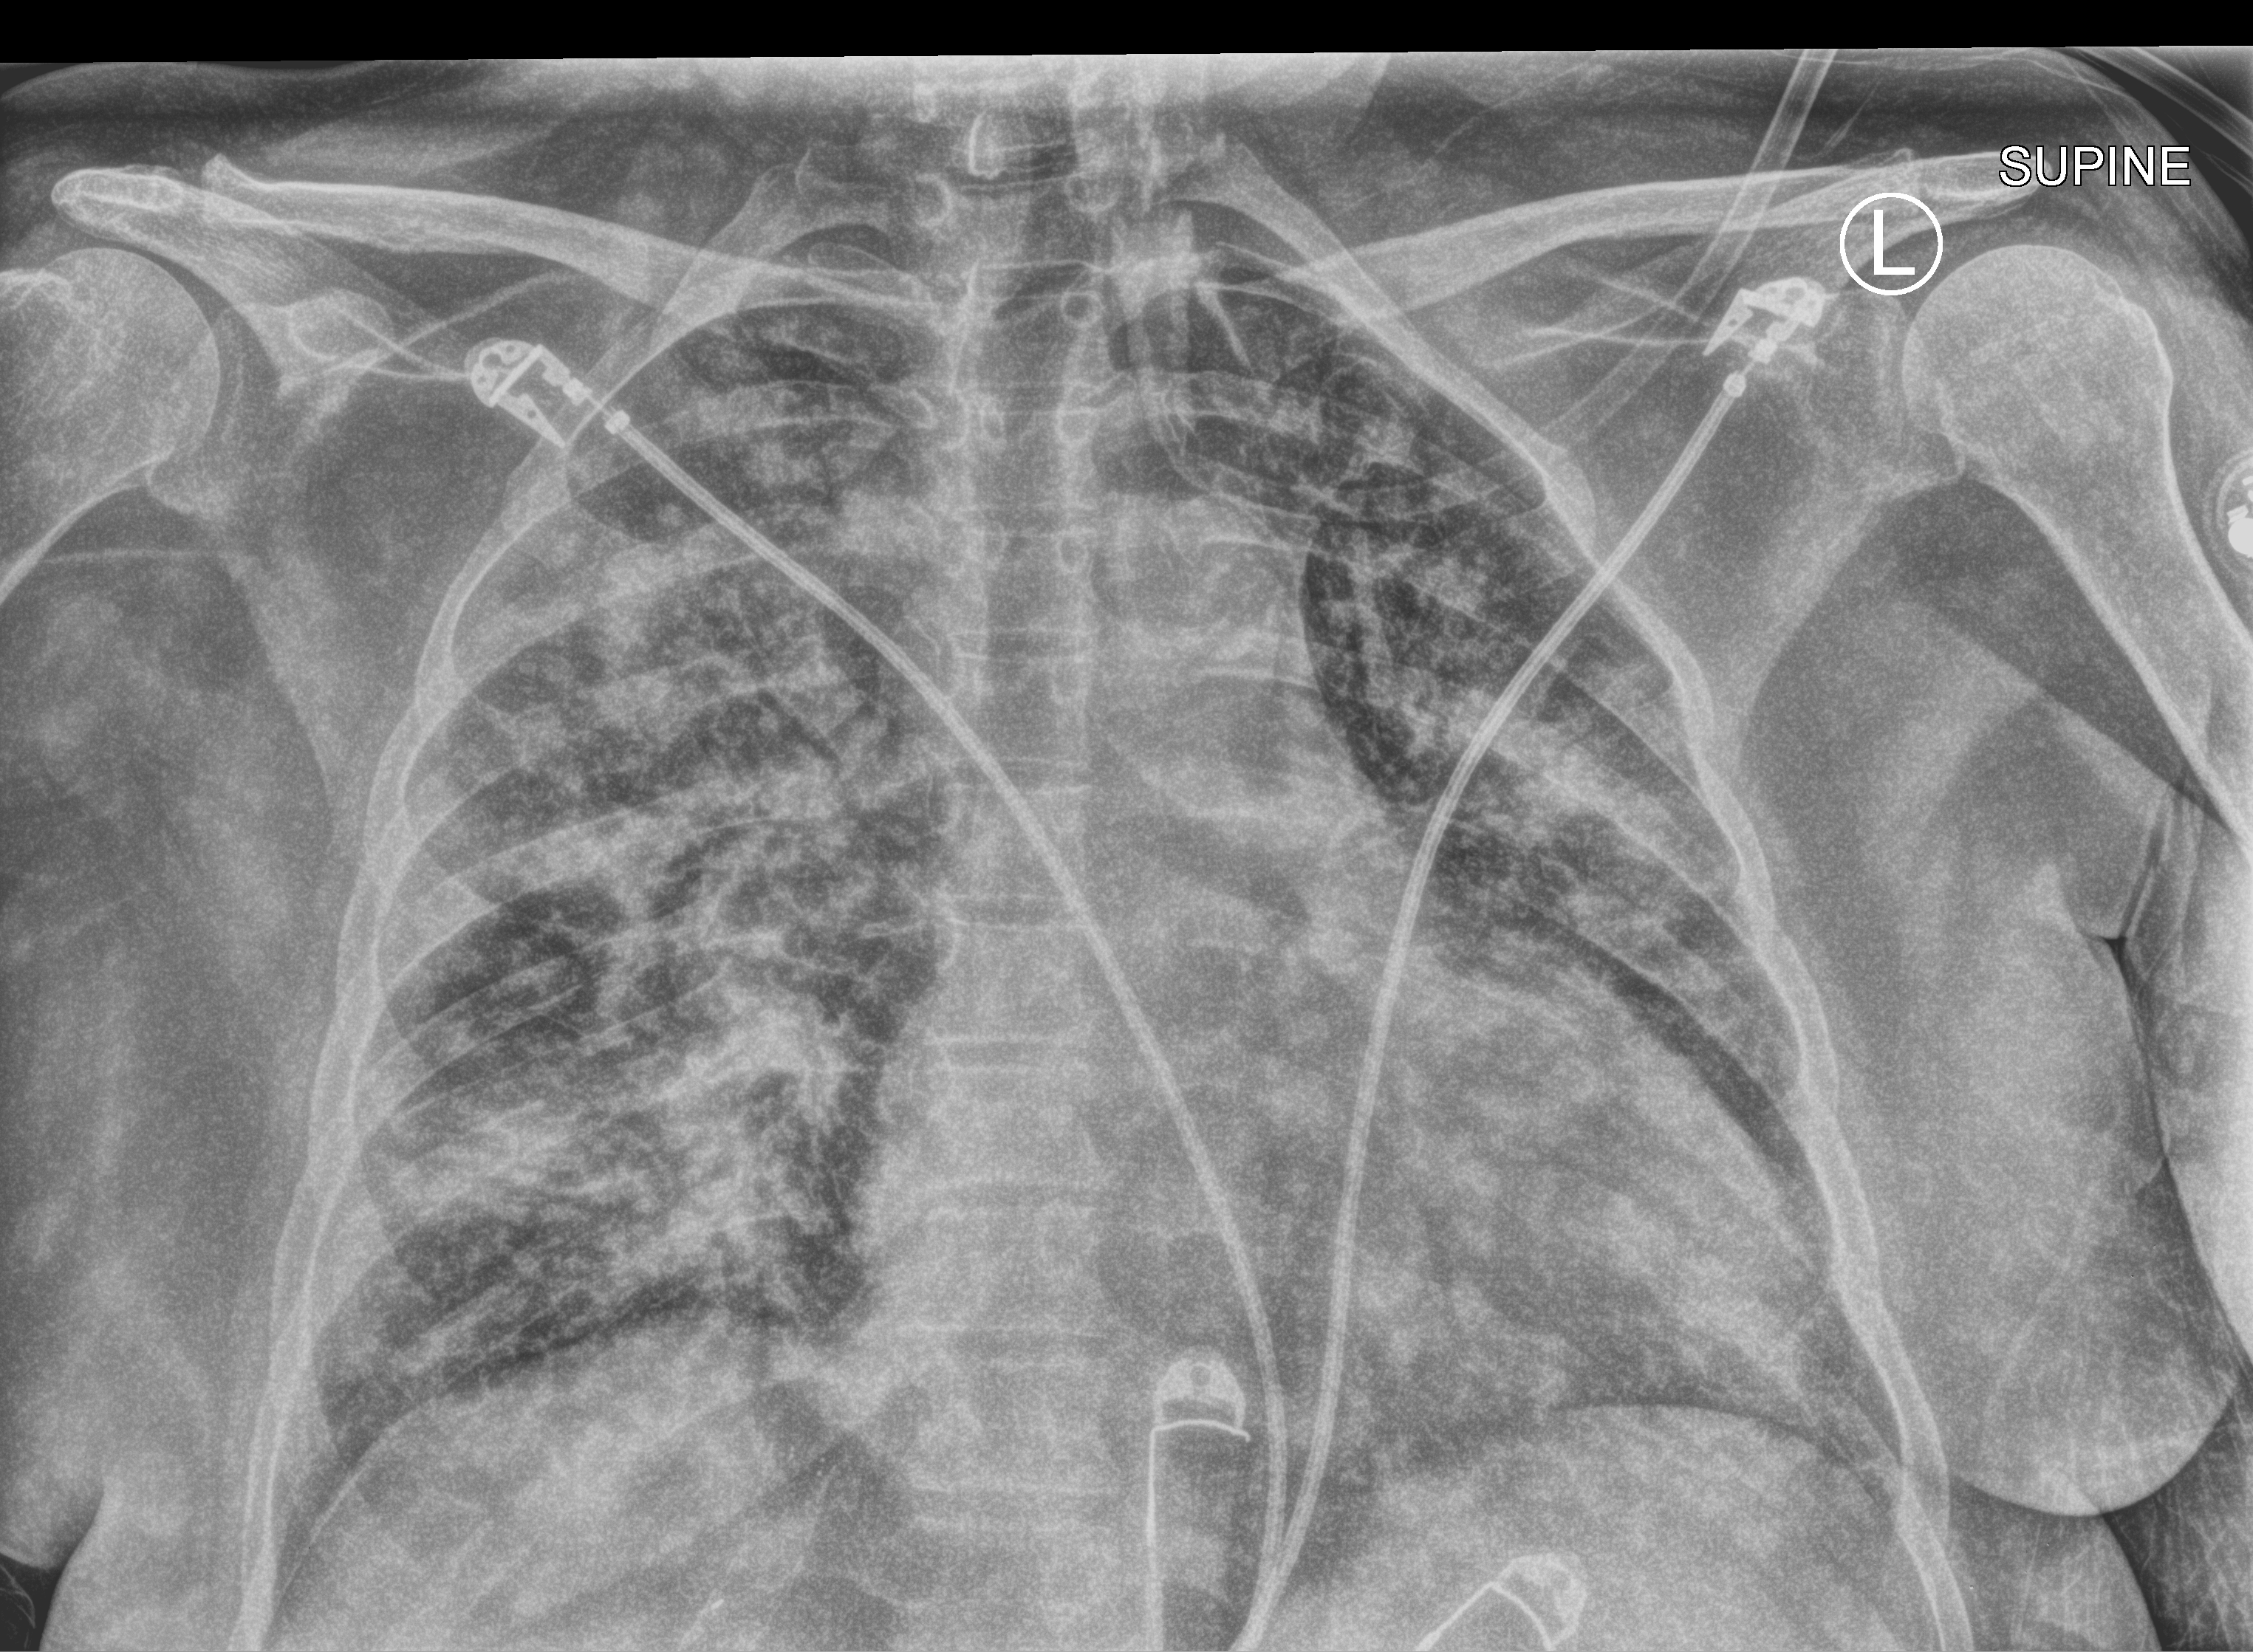
Portable chest radiograph; anteroposterior (AP) projection. Patient hospitalised with COVID-19; female, aged 60–74 years.
Hospital-stay facts (about this admission, not read from this image; timing relative to this image not recorded):
- length of hospital stay: 17 days